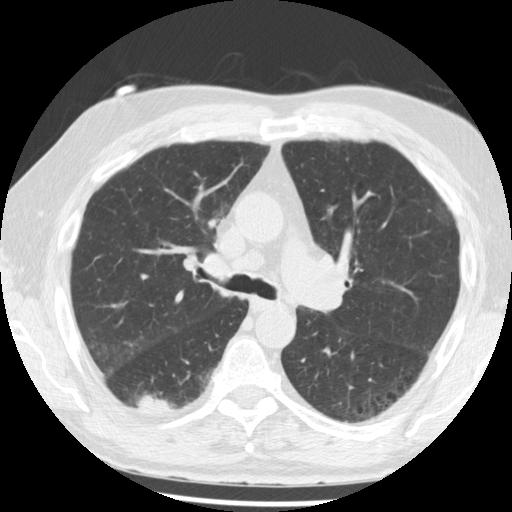
Low-dose screening chest CT, one axial slice; position 134 of 221 along the scan axis; 120 kVp; lung window (W 1500 / L -600 HU); 2.5 mm slice thickness; 512 × 512 image matrix, field of view 350 × 350 mm.
Annotated regions visible in this slice (outlined manually by an expert reader):
- lesion 1 (tumor, lower lobe of right lung): bounding box (x1, y1, x2, y2) in pixels: (137, 395, 176, 413)